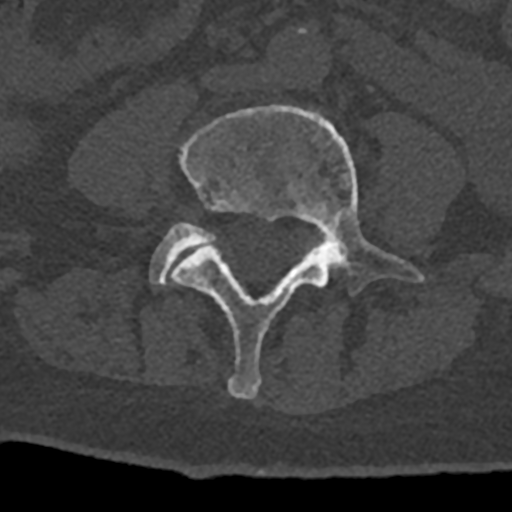
CT including the spine, one axial slice. Slice 248 of 797 in the series (ordered by position). Reconstruction kernel Br40s/3. 120 kVp. Bone window (W 1800 / L 400 HU). 512 × 512 image matrix, field of view 160 × 160 mm. Male patient, age 74 years. Case-level facts recorded for this patient, not image findings: primary cancer: renal; vertebrae with lytic lesions (as recorded): T10, L1, L2, L3, L4, L5.
Structures marked on this image (semi-automatically segmented with operator editing):
- L4 vertebra: bounding box <171,105,424,399> (left, top, right, bottom; pixels)
- L5 vertebra: <150,223,216,286>